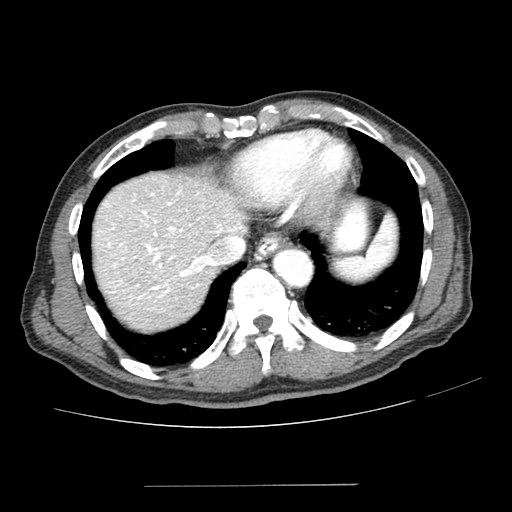
Contrast-enhanced abdominal CT (liver protocol), one axial slice; slice 174 of 187 in the series (ordered by position); one of 2 acquisitions stored at this slice position; soft-tissue window (W 400 / L 40 HU); 512 × 512 image matrix, field of view 360 × 360 mm. From the clinical record (not read from this slice): diagnosis: hepatocellular carcinoma (patient treated with transarterial chemoembolisation; whether this scan precedes or follows treatment is not stated here); TNM stage (as recorded): Stage-I; Child-Pugh class: A; tumour size: 1.6 cm.
Outlined on this slice (semi-automatic segmentation, software-assisted and operator-edited):
- abdominal aorta: bounding box (x1, y1, x2, y2) in pixels: (273, 248, 312, 286)
- liver parenchyma outside the tumour (the mass and vessels are separate outlines, so this box may not span the whole liver): (94, 172, 246, 330)
- mass: (117, 259, 152, 285)
- liver vessels: (105, 191, 241, 299)